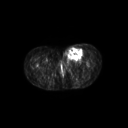
FDG PET of an extremity soft-tissue mass (from a PET/CT study), one axial slice. Position 49 of 267 along the scan axis. 128 × 128 image matrix, field of view 600 × 600 mm. Female patient, age 24 years. Case-level facts recorded for this patient, not image findings: histological type: leiomyosarcoma; grade: high; site of the primary tumour: groin.
Annotated regions visible in this slice (expert contour drawn on MRI and transferred to this co-registered scan by the dataset authors):
- gross tumour volume including surrounding oedema: box from (x=62, y=46) to (x=83, y=62) px
- gross tumour volume (mass): (x=67, y=48)–(x=83, y=59)